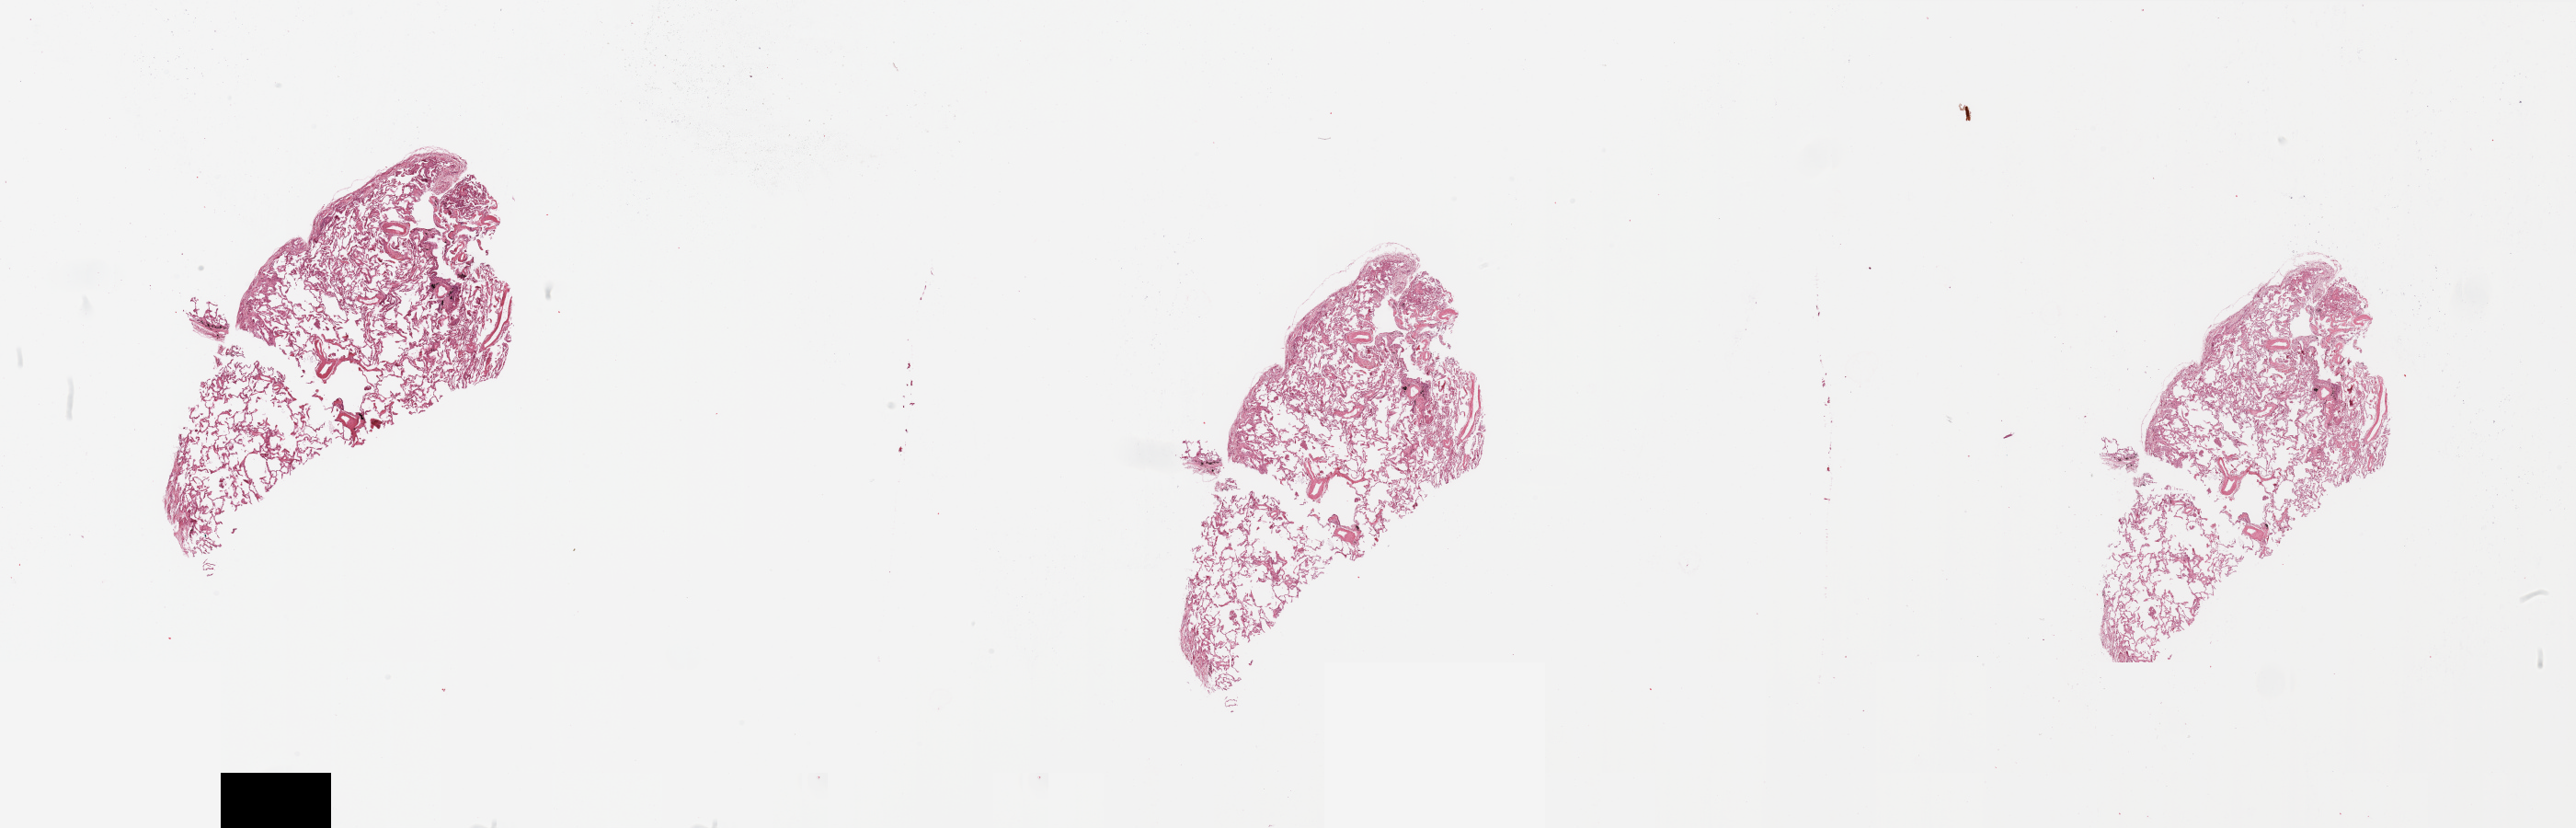
Digitized Hematoxylin and eosin (H&E) stained tissue section (whole slide), low-resolution overview of the scanned area, about 44.3 x 14.2 mm; normal (non-tumour) tissue sample, sampled site: lung. Patient: male, age 73 years.
- this section: normal (non-tumour) tissue from the same patient
- patient diagnosis: Squamous cell carcinoma, NOS